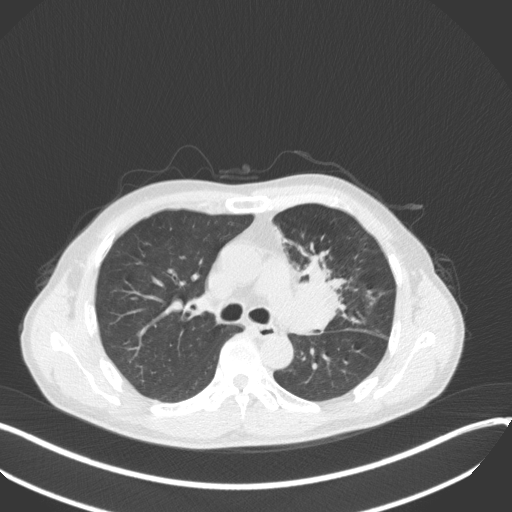
Chest CT, one axial slice. Slice 214 of 411 in the series (ordered by position). Reconstruction kernel B31f. 120 kVp. Lung window (W 1500 / L -600 HU). 1 mm slice thickness. 512 × 512 image matrix. Male patient, age 56 years. From the clinical record (not read from this slice): clinical TNM (as recorded): T2a N0 M0.
Outlined on this slice (bounding box drawn by a radiologist):
- lung tumour (recorded histology: squamous cell carcinoma): bounding box [x1, y1, x2, y2] px = [291, 249, 348, 339]